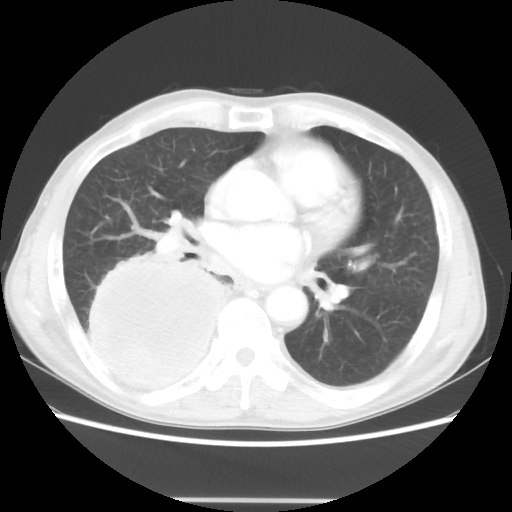
Chest CT, one axial slice. Lung window (W 1500 / L -600 HU). 512 × 512 image matrix, field of view 361 × 361 mm. Patient: male, 66 years. Case-level facts recorded for this patient, not image findings: clinical TNM (as recorded): T4 N1 M1; histopathological grade: G3.
Outlined on this slice (rectangle marked by the reading radiologist):
- lung tumour (recorded histology: small cell carcinoma): bounding box [x1, y1, x2, y2] px = [80, 253, 224, 400]